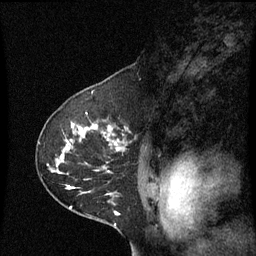
Breast MRI (dynamic contrast-enhanced), one sagittal slice. Position 43 of 60 along the scan axis. Dynamic contrast-enhanced series, image 2 of 3 at this slice position (ordered by acquisition). 1.5 T. TE 4.2 ms, TR 8.9 ms. 256 × 256 image matrix, field of view 200 × 200 mm. Patient: female, 53 years. Case-level facts recorded for this patient, not image findings: setting: breast cancer imaged before/during neoadjuvant chemotherapy; receptor status: HR-positive, HER2-negative.
Outlined on this slice (semi-automatically segmented with operator editing):
- analysis volume of interest (the breast-tissue region the enhancement analysis was run in; not a lesion): bounding box (x1, y1, x2, y2) in pixels: (40, 102, 145, 221)
- tumour enhancement mask (voxels above the 70 % enhancement threshold inside the analysis volume of interest): (66, 124, 123, 215)